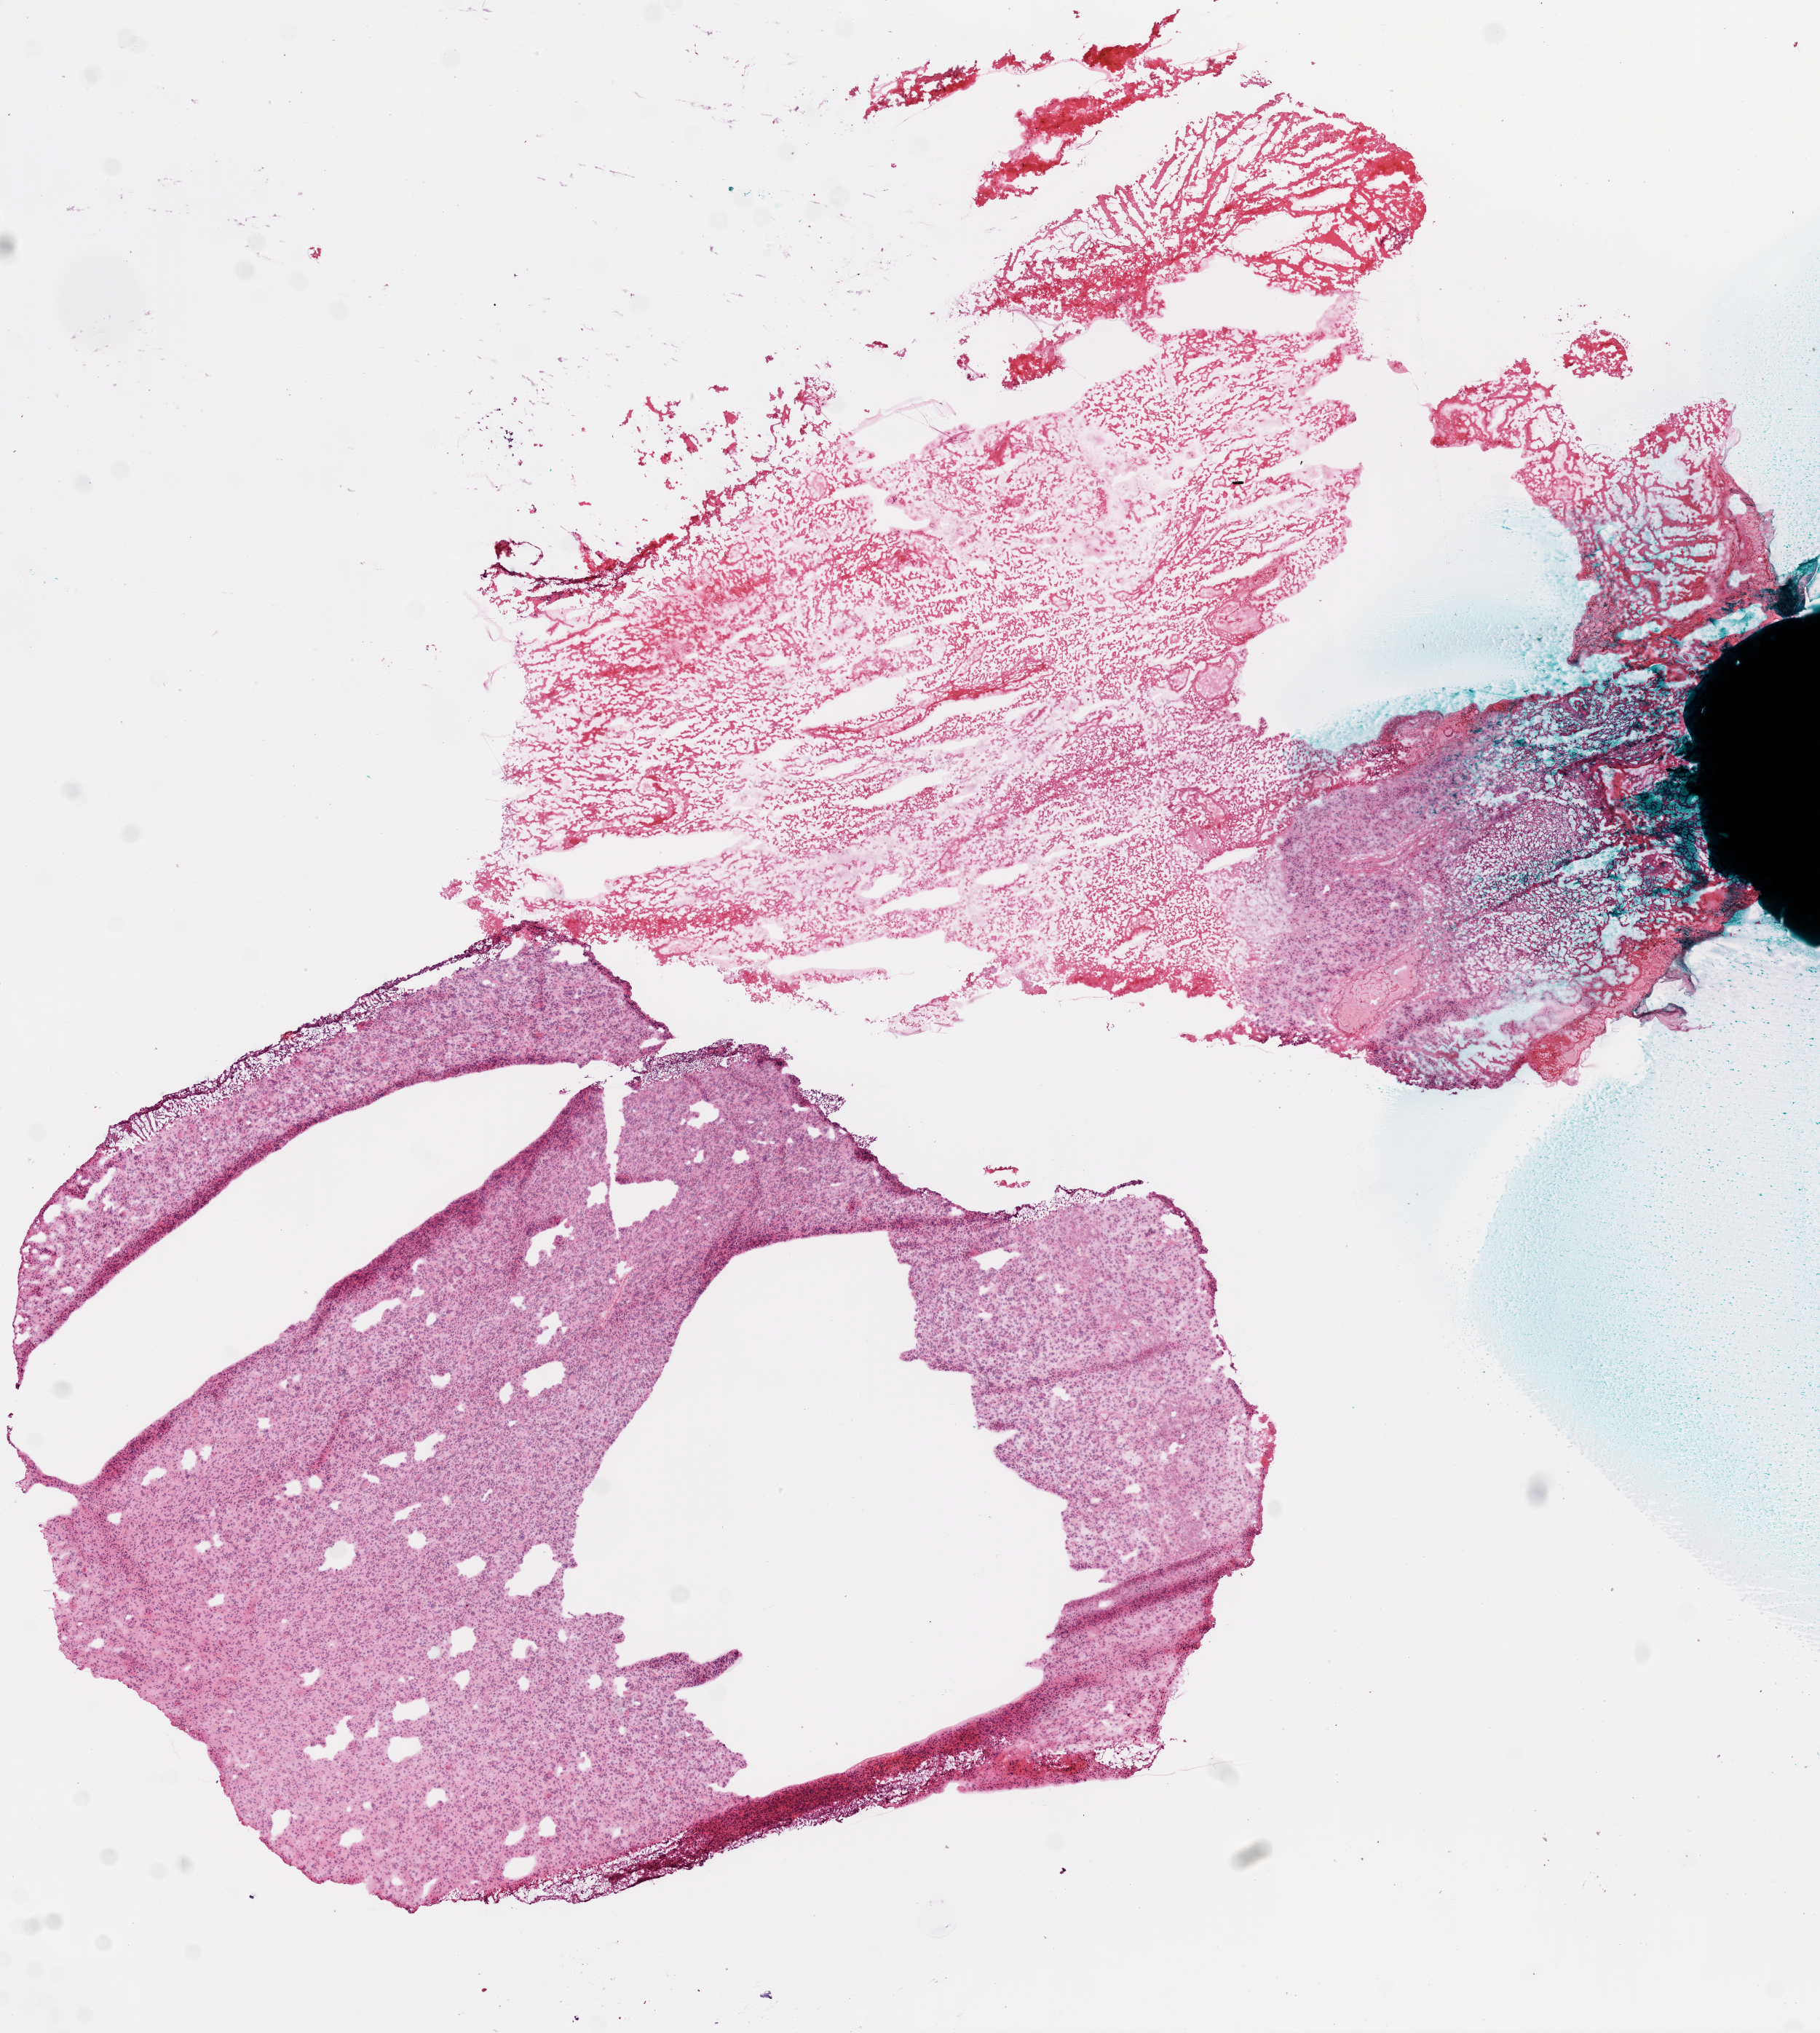
Hematoxylin and eosin (H&E) stained whole-slide image — shown as a low-resolution overview of the whole scanned area (about 10.0 x 11.2 mm, acquisition: 20x scan); frozen section from the bottom of the tissue portion; sample: primary tumour, brain. Male, age 69 years at initial diagnosis.
Histologic diagnosis: Glioblastoma.